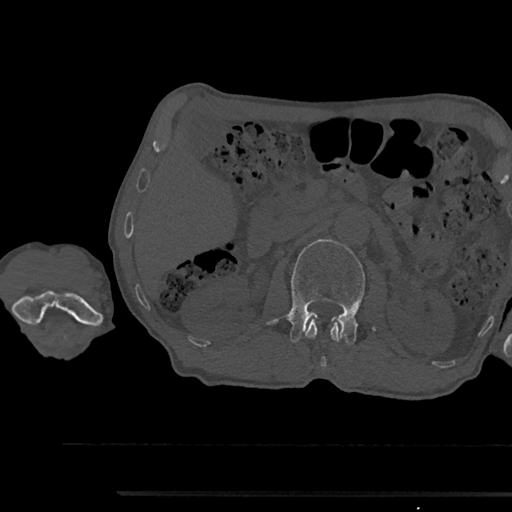
CT including the spine, one axial slice; reconstruction kernel Br40s/3; 120 kVp; bone window (W 1800 / L 400 HU); 0.5 mm slice thickness; 512 × 512 image matrix, field of view 367 × 367 mm. Male patient, age 79 years. From the clinical record (not read from this slice): primary cancer: prostate.
Structures marked on this image (semi-automatically segmented with operator editing):
- L1 vertebra: bounding box [x1, y1, x2, y2] px = [305, 319, 341, 367]
- L2 vertebra: [269, 239, 375, 345]